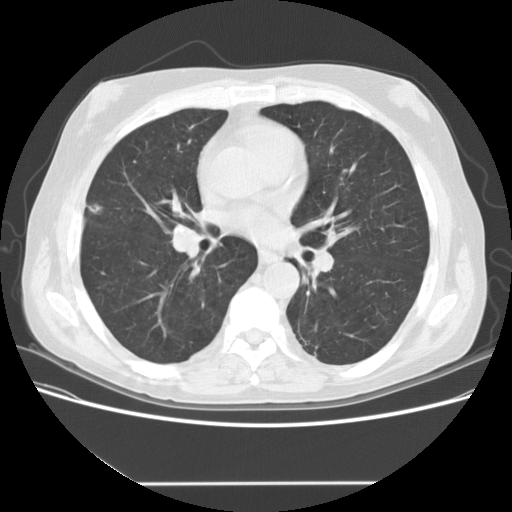
Low-dose screening chest CT, one axial slice. Slice 85 of 153 in the series (ordered by position). Reconstruction kernel STANDARD. Lung window (W 1500 / L -600 HU). 2.5 mm slice thickness. 512 × 512 image matrix, field of view 360 × 360 mm.
Annotated regions visible in this slice (outlined manually by an expert reader):
- lesion 2 (tumor, upper lobe of right lung): bounding box (x1, y1, x2, y2) in pixels: (89, 203, 103, 214)